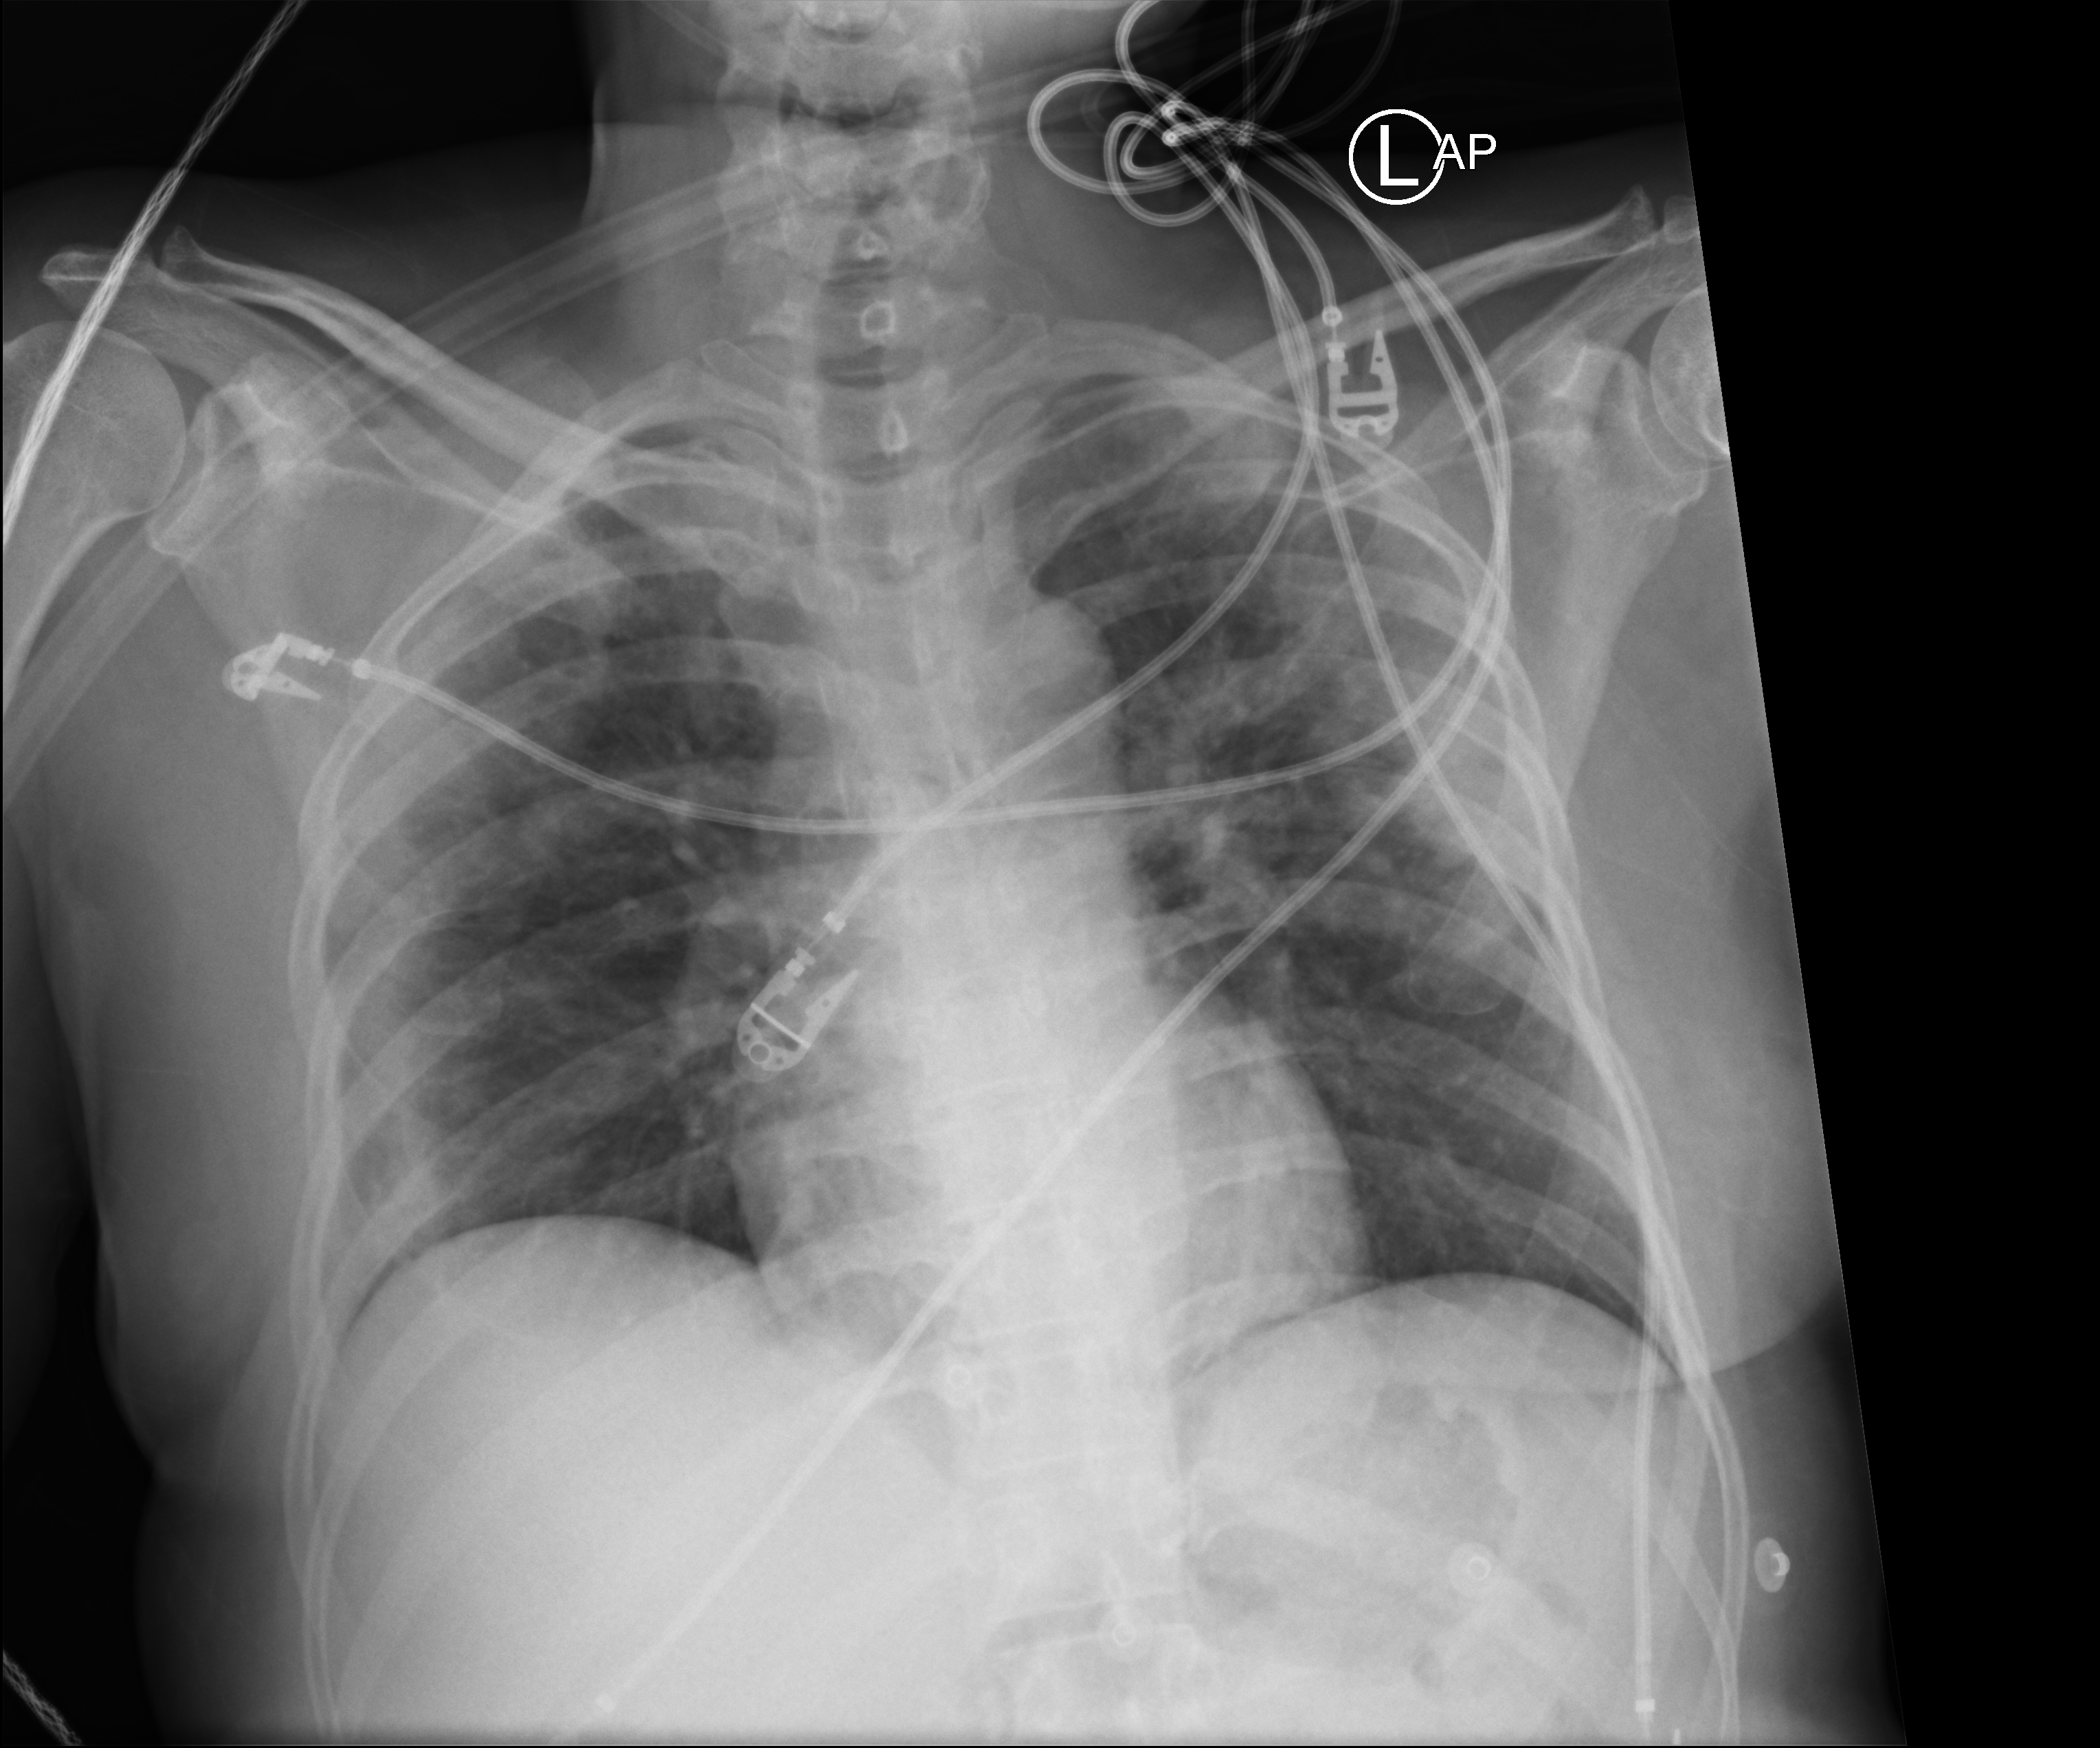
Portable chest radiograph, anteroposterior (AP) projection. Female patient hospitalised with COVID-19, age 18–59 years.
Hospital-stay facts (about this admission, not read from this image; timing relative to this image not recorded): length of hospital stay: 7 days; COPD (admission record): no.